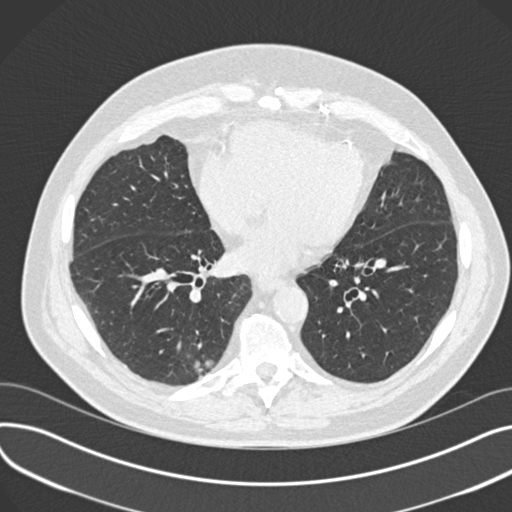
Axial slice from a low-dose chest CT screening exam, third screening round (two years after baseline), lung window (W 1500 / L -600 HU), 512 × 512 image matrix. Male, age 68 years at enrolment.
Lesion marked by an expert reader, bounding box <174,345,218,384> (left, top, right, bottom; pixels). The screening reader recorded 4 non-calcified nodules or masses ≥4 mm on this exam; which of them this box marks is not recorded. Lung cancer was diagnosed 68 days after this screen: adenosquamous carcinoma, right lower lobe, moderately differentiated (G2), stage IB (AJCC 6th edition), 31 mm at pathology.